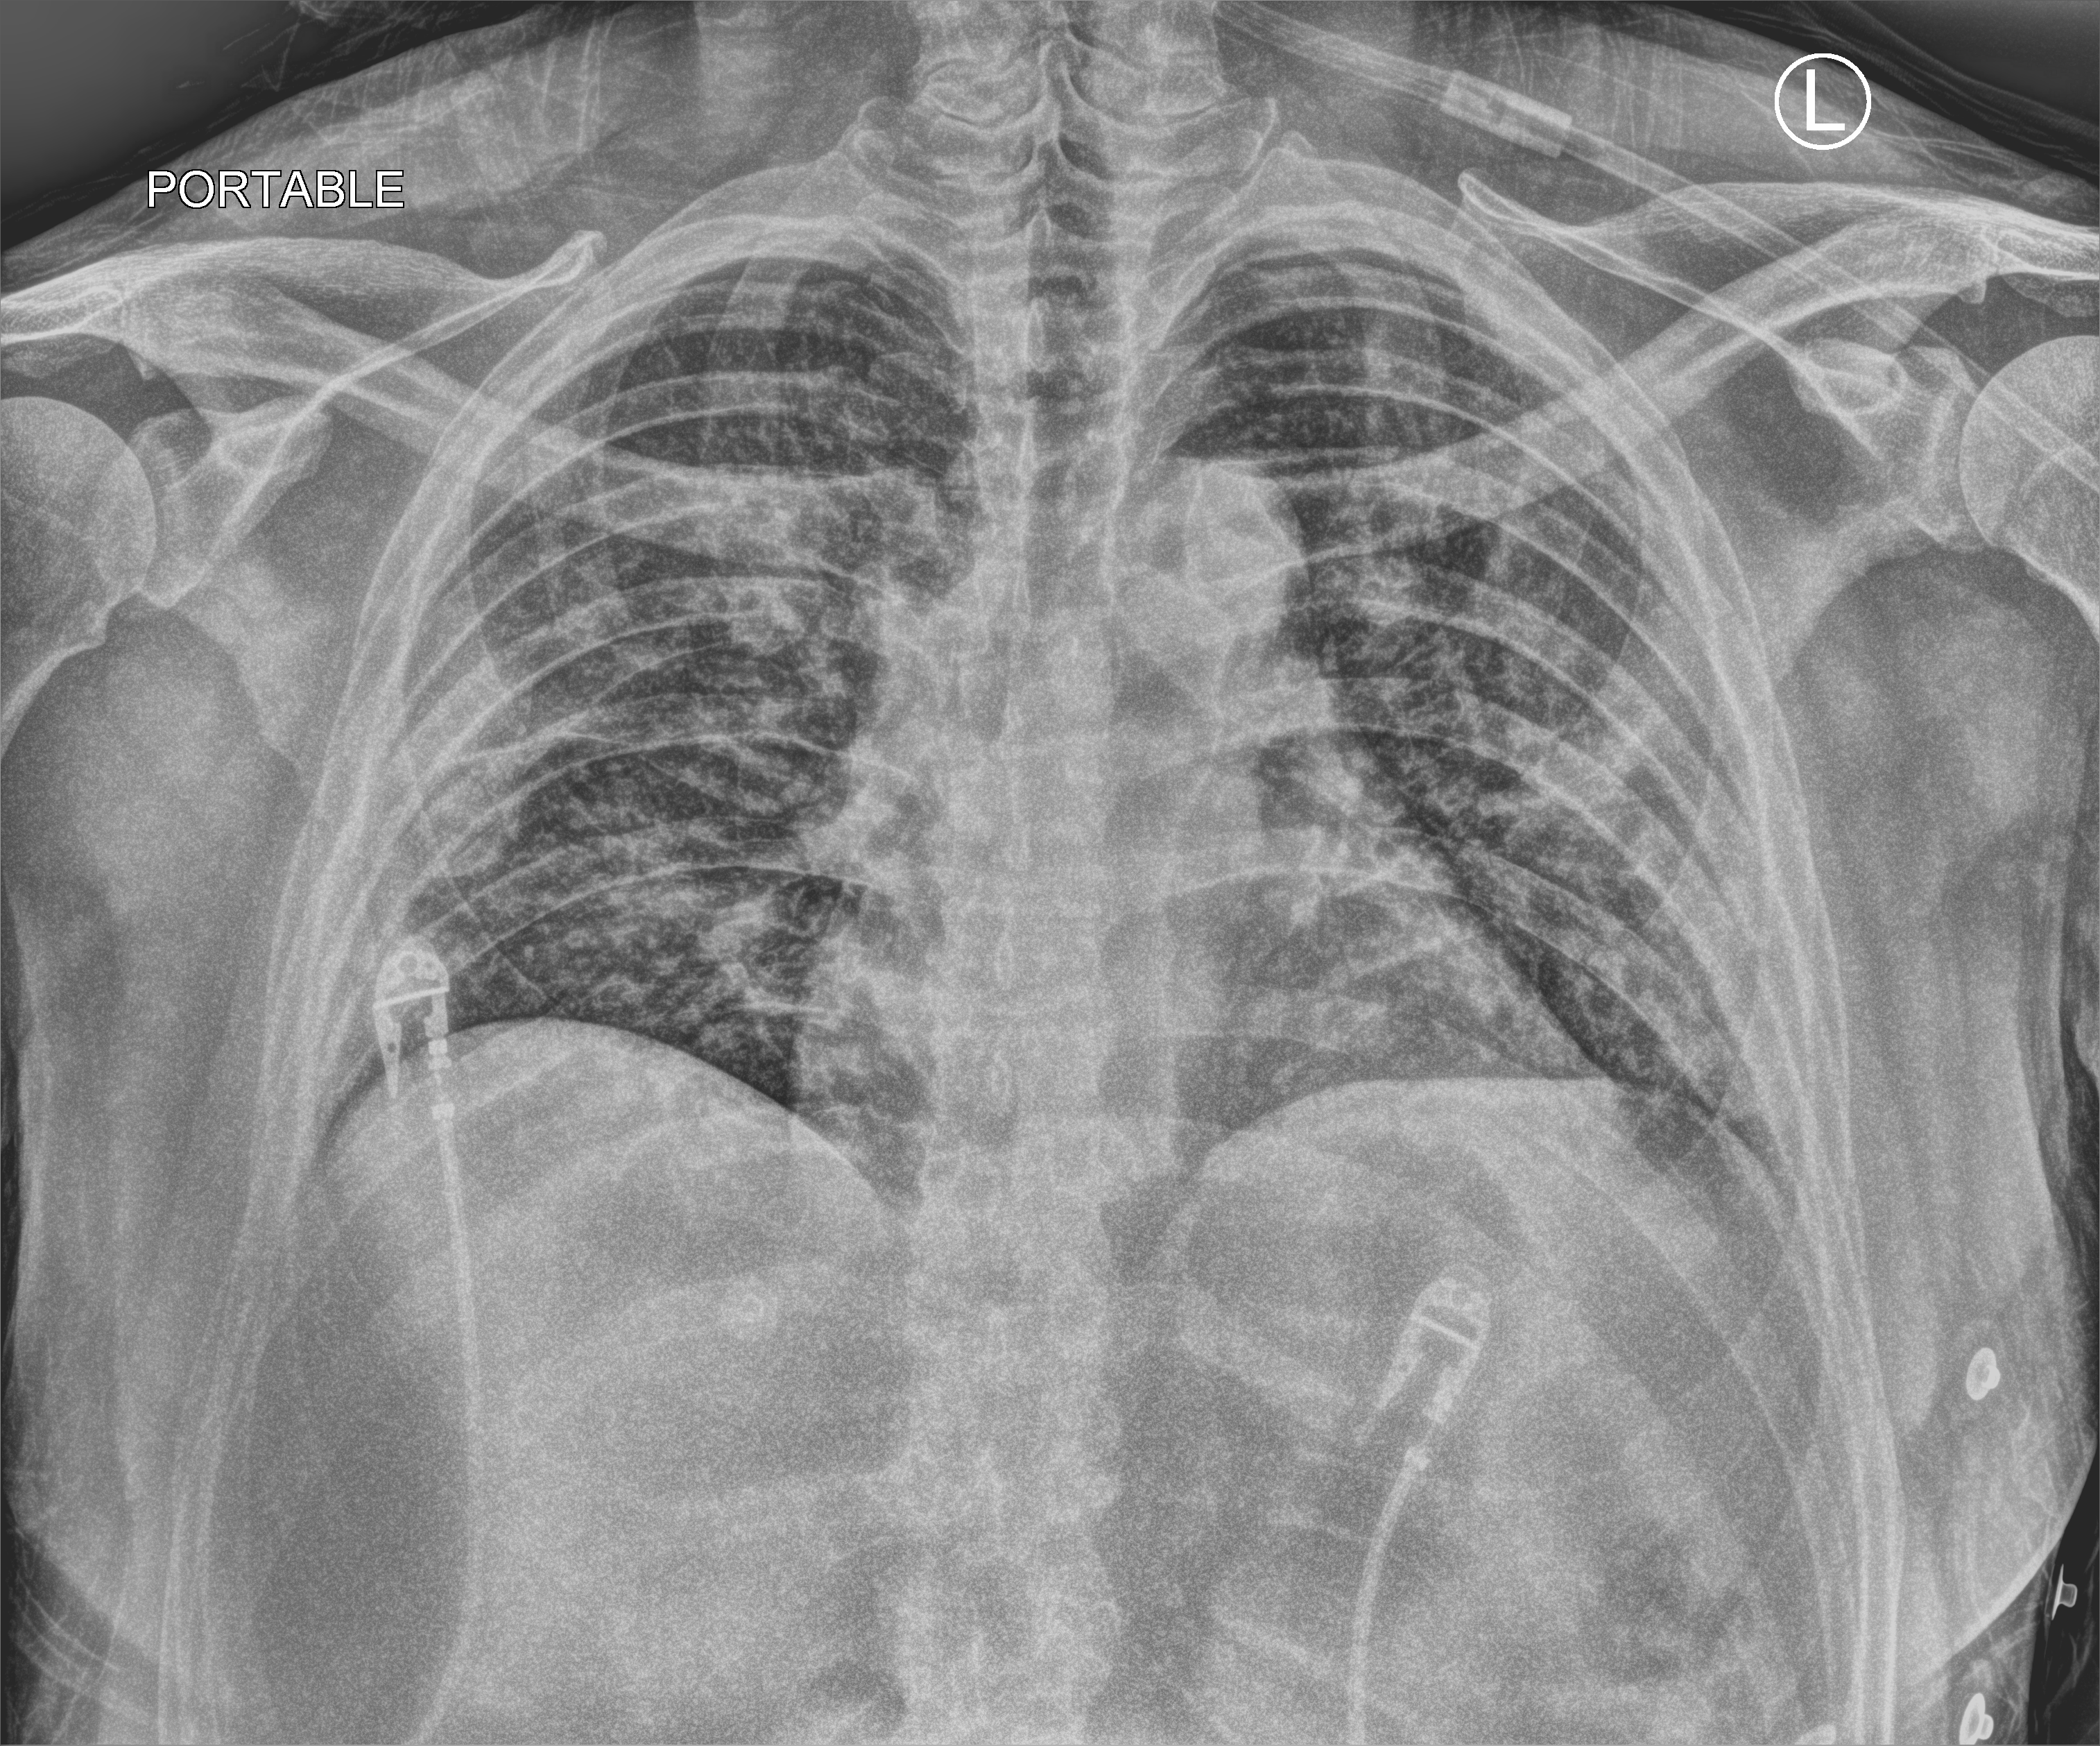
Chest X-ray (portable). Patient hospitalised with COVID-19; male, aged 18–59 years.
Hospital-stay facts (about this admission, not read from this image; timing relative to this image not recorded): mechanically ventilated during this hospital stay: no; admitted to intensive care during this hospital stay: yes; diabetes (admission record): no.